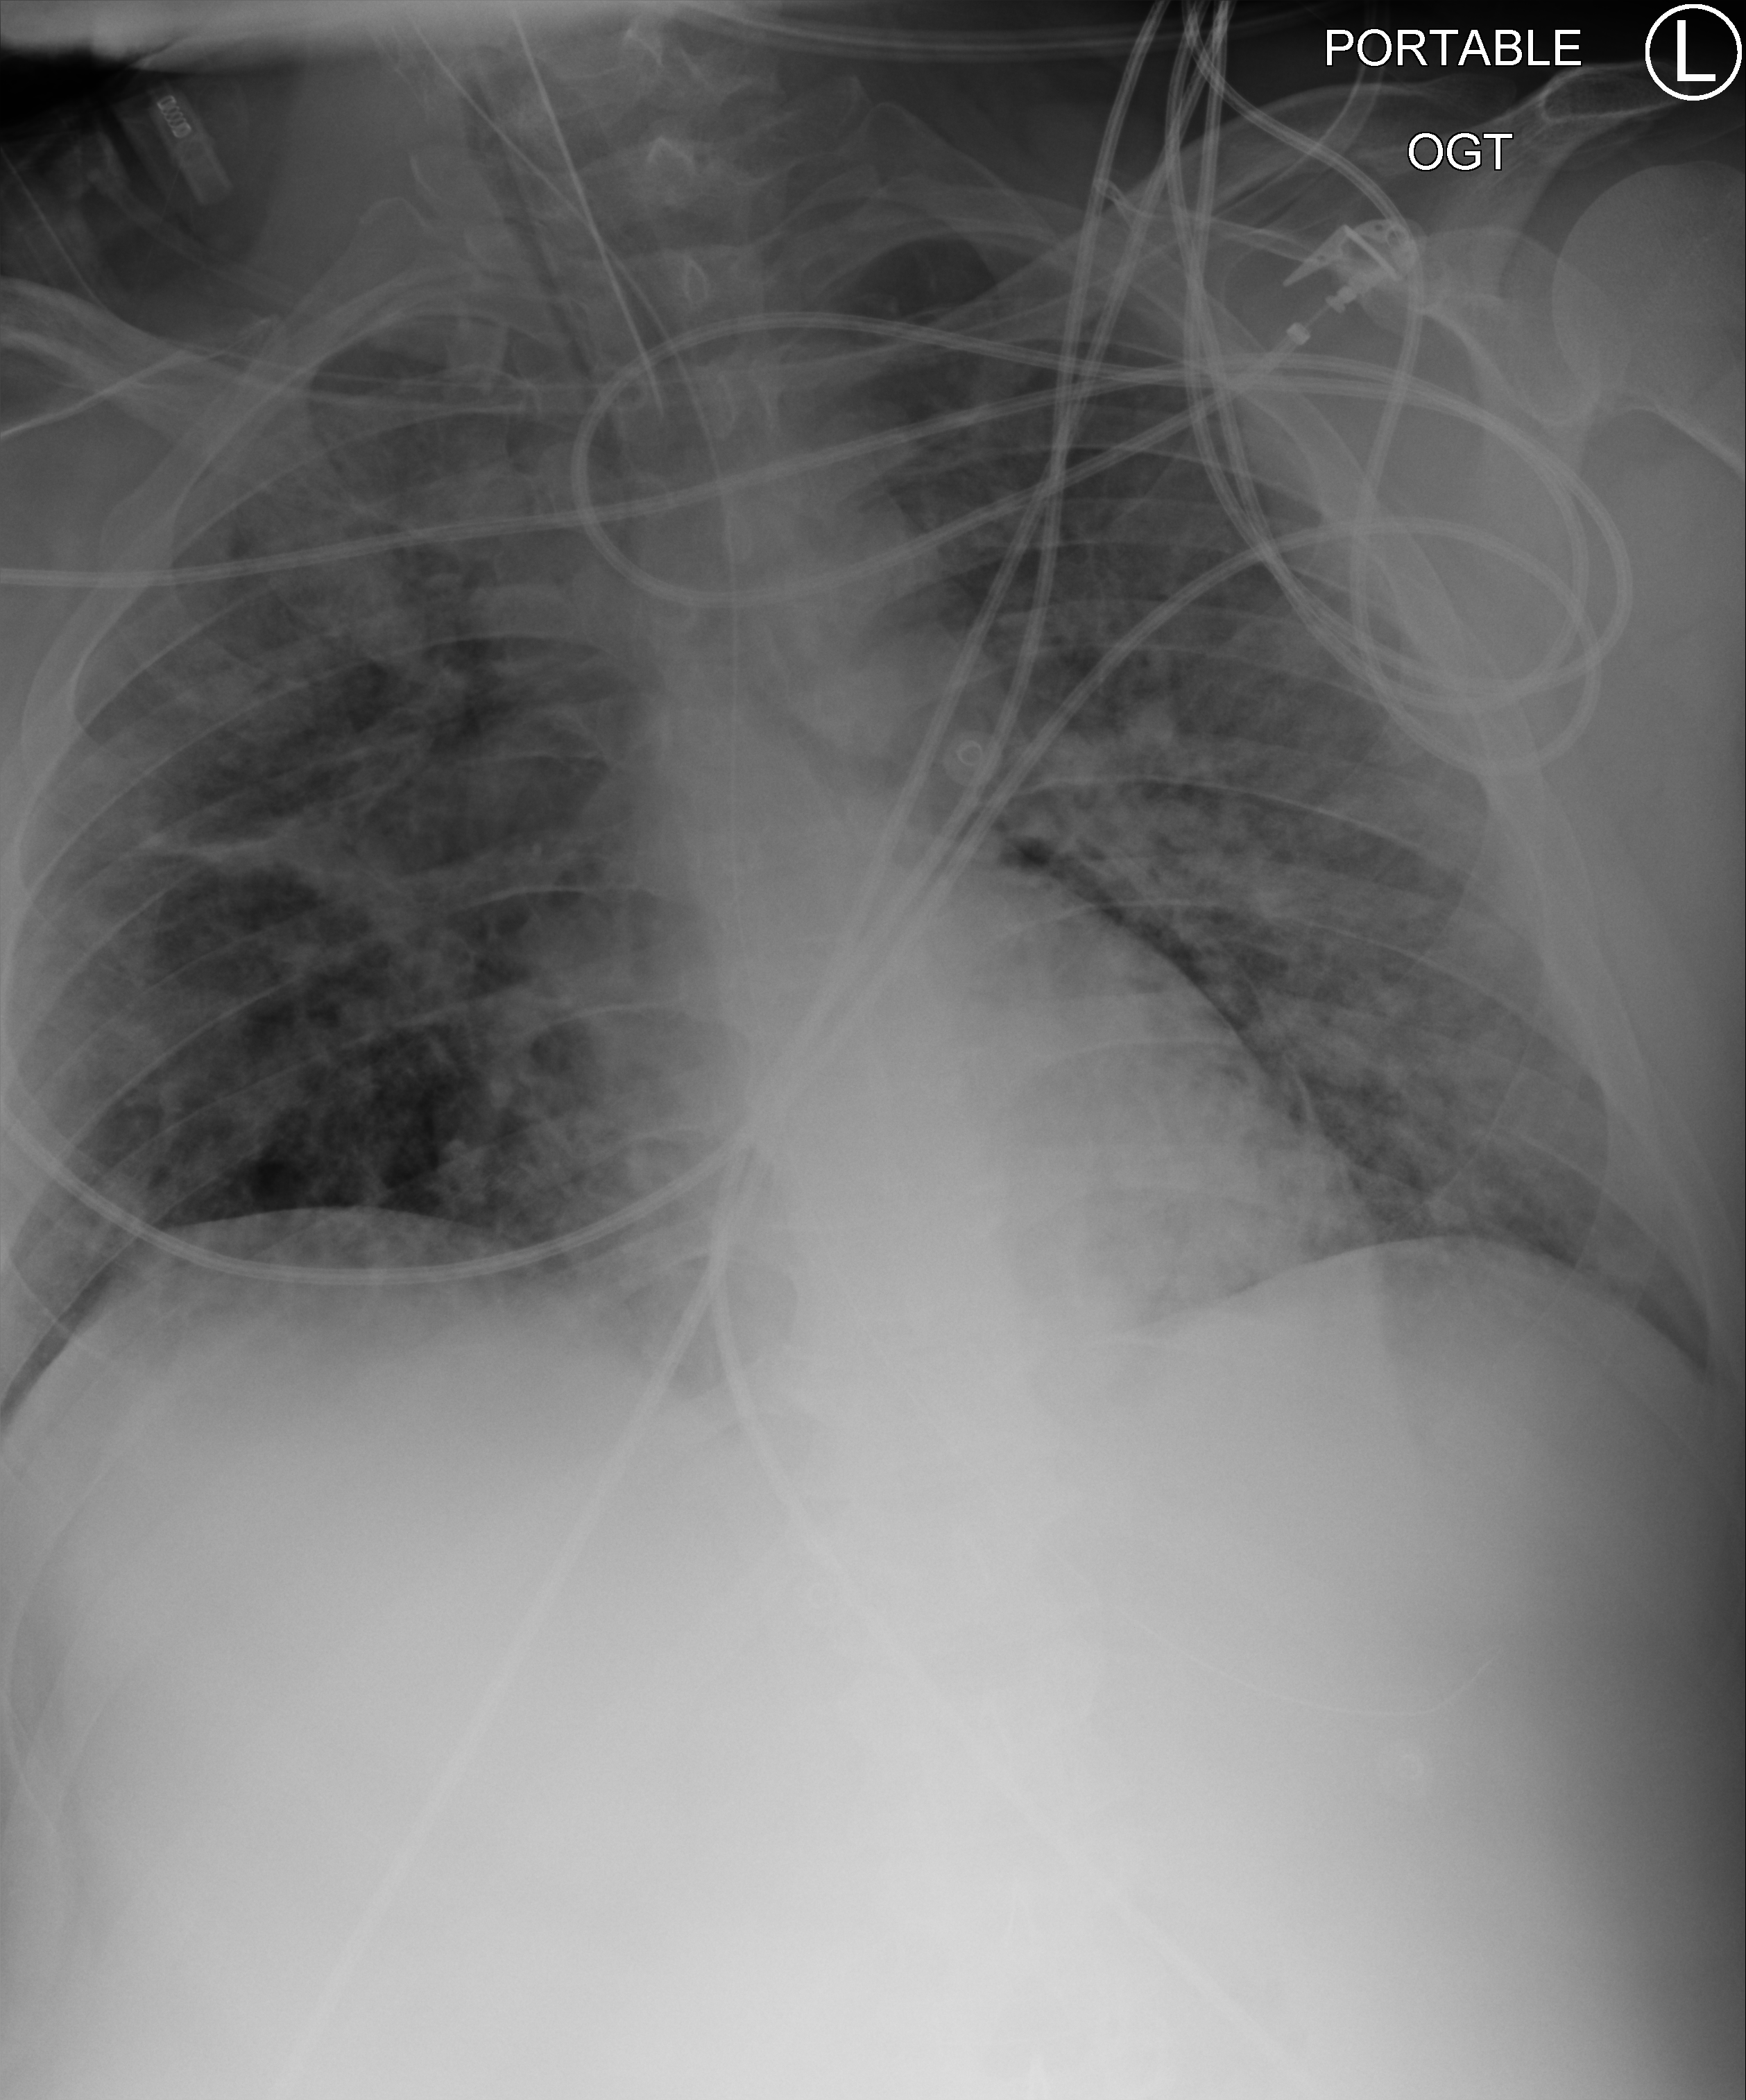
Chest X-ray (portable), anteroposterior (AP) projection. Adult patient hospitalised with COVID-19, age 18–59 years.
Hospital-stay facts (about this admission, not read from this image; timing relative to this image not recorded):
- length of hospital stay: 31 days
- admitted to intensive care during this hospital stay: yes
- mechanically ventilated during this hospital stay: yes